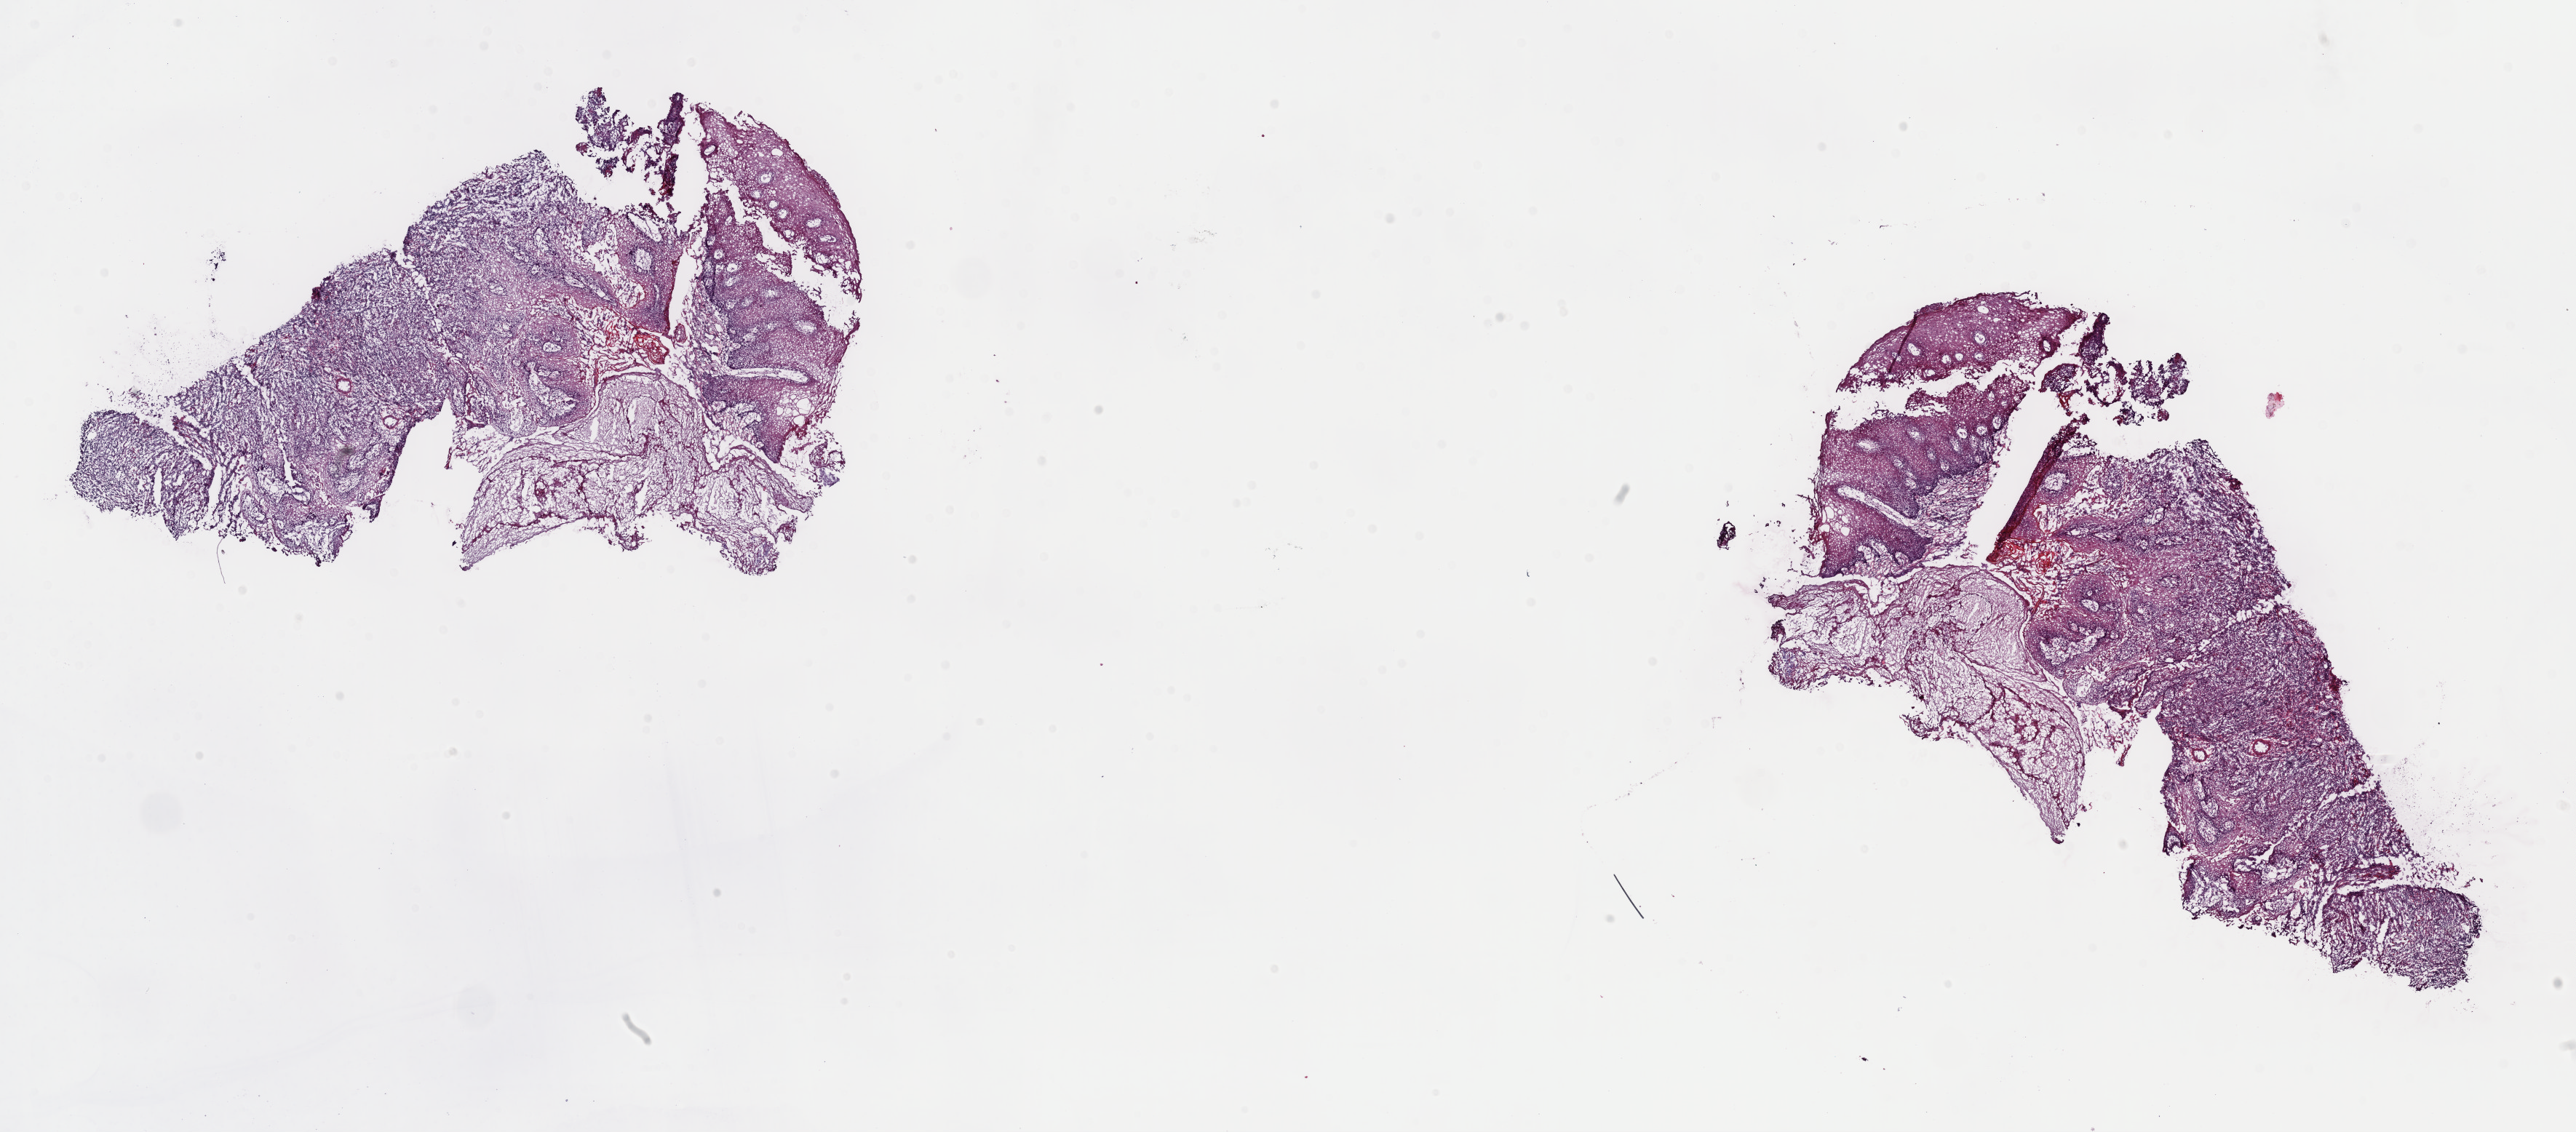
H&E whole-slide image, a low-resolution overview of the entire scanned area, about 28.0 x 12.3 mm, frozen section from the top of the tissue portion, primary tumour sample from the head and neck. Female patient; age at initial diagnosis 82 years. Histologic grade: G2 (moderately differentiated). Pathologist review of this section (percent, as recorded): tumour cells 80%, tumour nuclei 80%, normal cells 15%, stromal cells 5%, necrosis 0%. Infiltration values recorded for this section: lymphocyte infiltration 5%, monocyte infiltration 0%, neutrophil infiltration 0%.
AJCC pathologic stage: I. Histologic diagnosis: Squamous cell carcinoma, NOS (tongue, NOS).